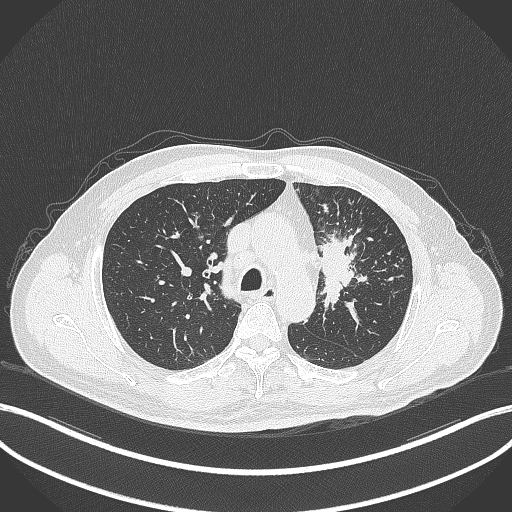
Chest CT, one axial slice; slice 245 of 386 in the series (ordered by position); reconstruction kernel B70f; lung window (W 1500 / L -600 HU); 1 mm slice thickness; 512 × 512 image matrix, field of view 400 × 400 mm. Male patient, age 69 years. Case-level facts recorded for this patient, not image findings: clinical TNM (as recorded): T2a N2 M0.
Structures marked on this image (rectangle marked by the reading radiologist):
- lung tumour (recorded histology: adenocarcinoma): bounding box <312,228,369,311> (left, top, right, bottom; pixels)